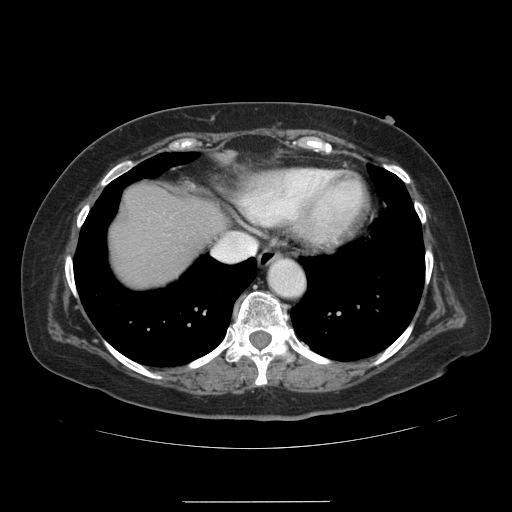
Contrast-enhanced abdominal CT, one axial slice. Slice 123 of 141 in the series (ordered by position). 120 kVp. Intravenous contrast given. Soft-tissue window (W 400 / L 40 HU). 2.5 mm slice thickness. 512 × 512 image matrix. Female patient, age 74 years. From the clinical record (not read from this slice): diagnosis: colorectal cancer liver metastases, imaged before liver resection.
Structures marked on this image (manually delineated by an expert):
- liver: bounding box <110,187,224,288> (left, top, right, bottom; pixels)
- planned liver remnant (the part of the liver to remain after resection): <110,187,224,288>